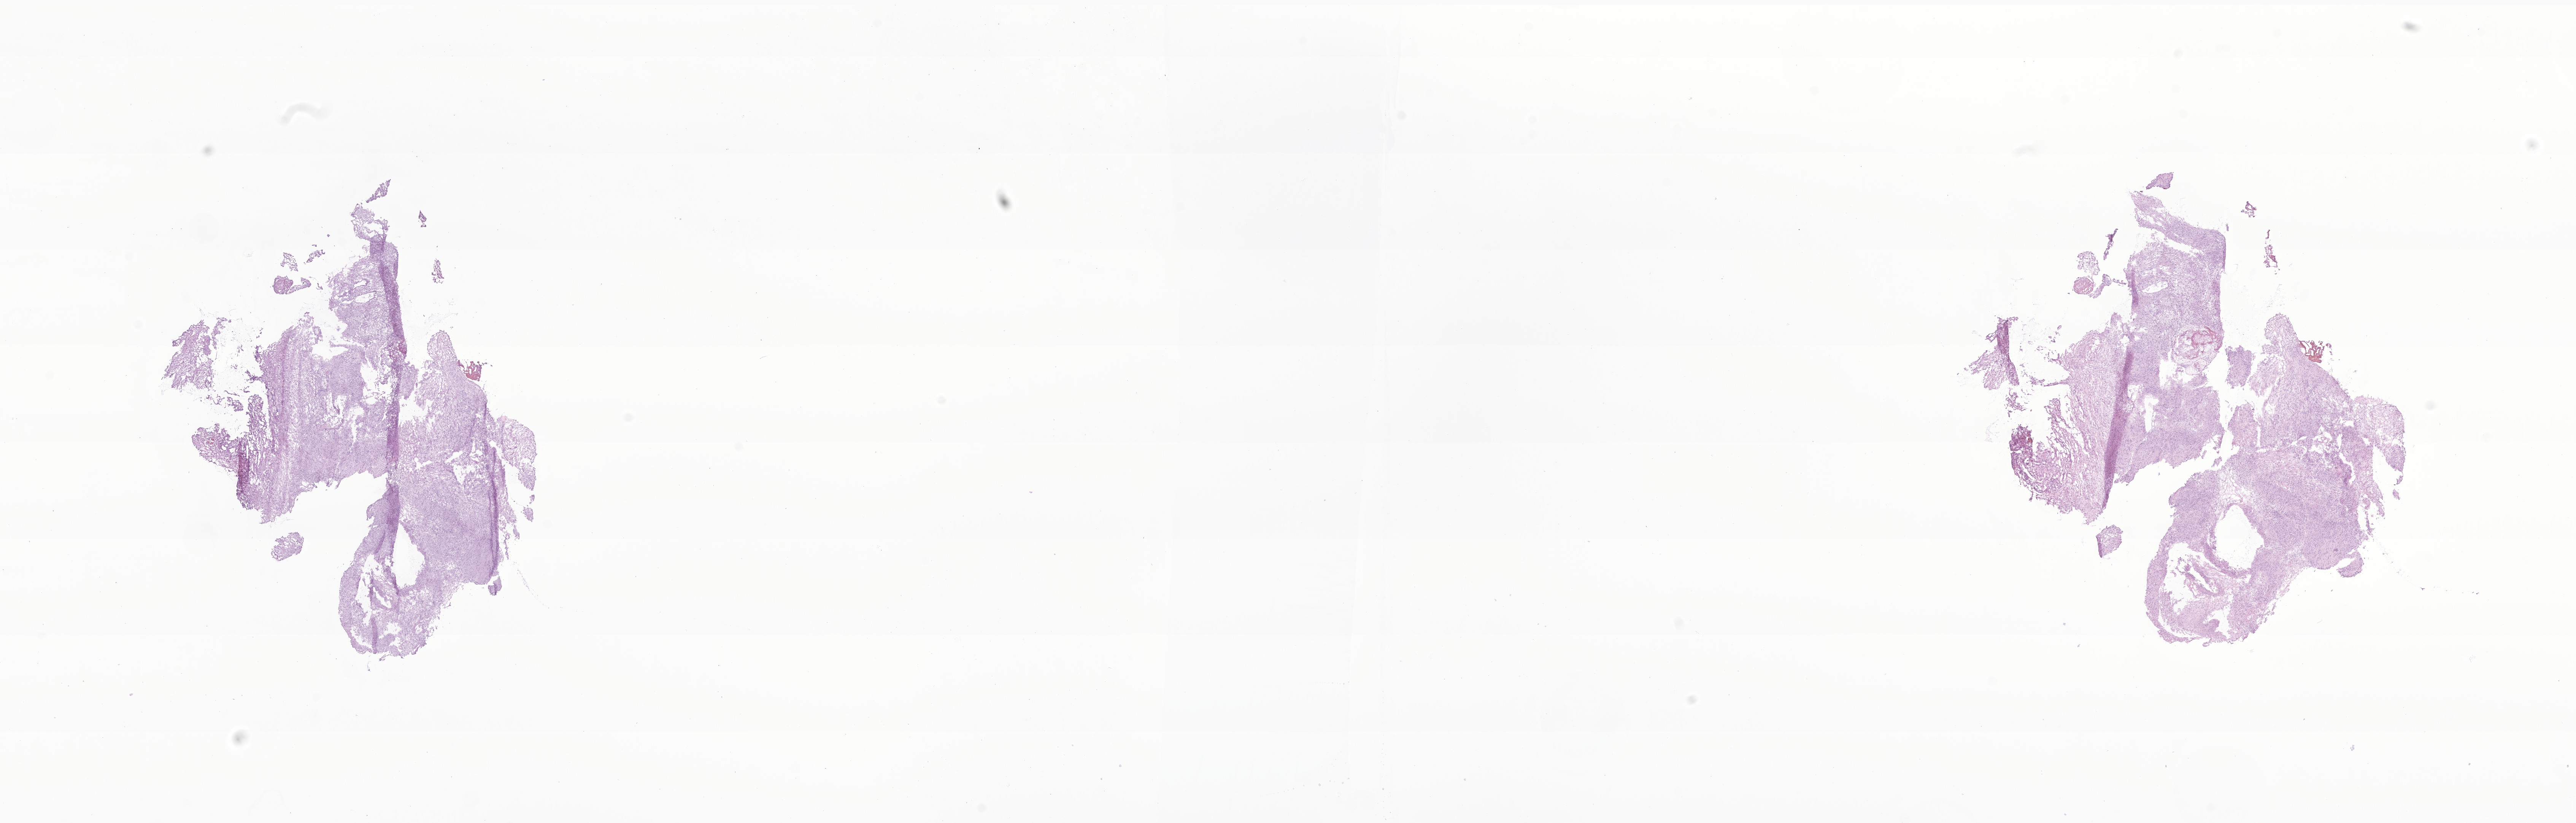
Whole-slide image, haematoxylin and eosin stain of tumor tissue from the brain, whole scanned area (about 28.6 x 9.1 mm) shown as a low-resolution overview; frozen section. Male patient, age 142 months (11 years 10 months).
• recorded diagnosis: Malignant tumor, spindle cell type